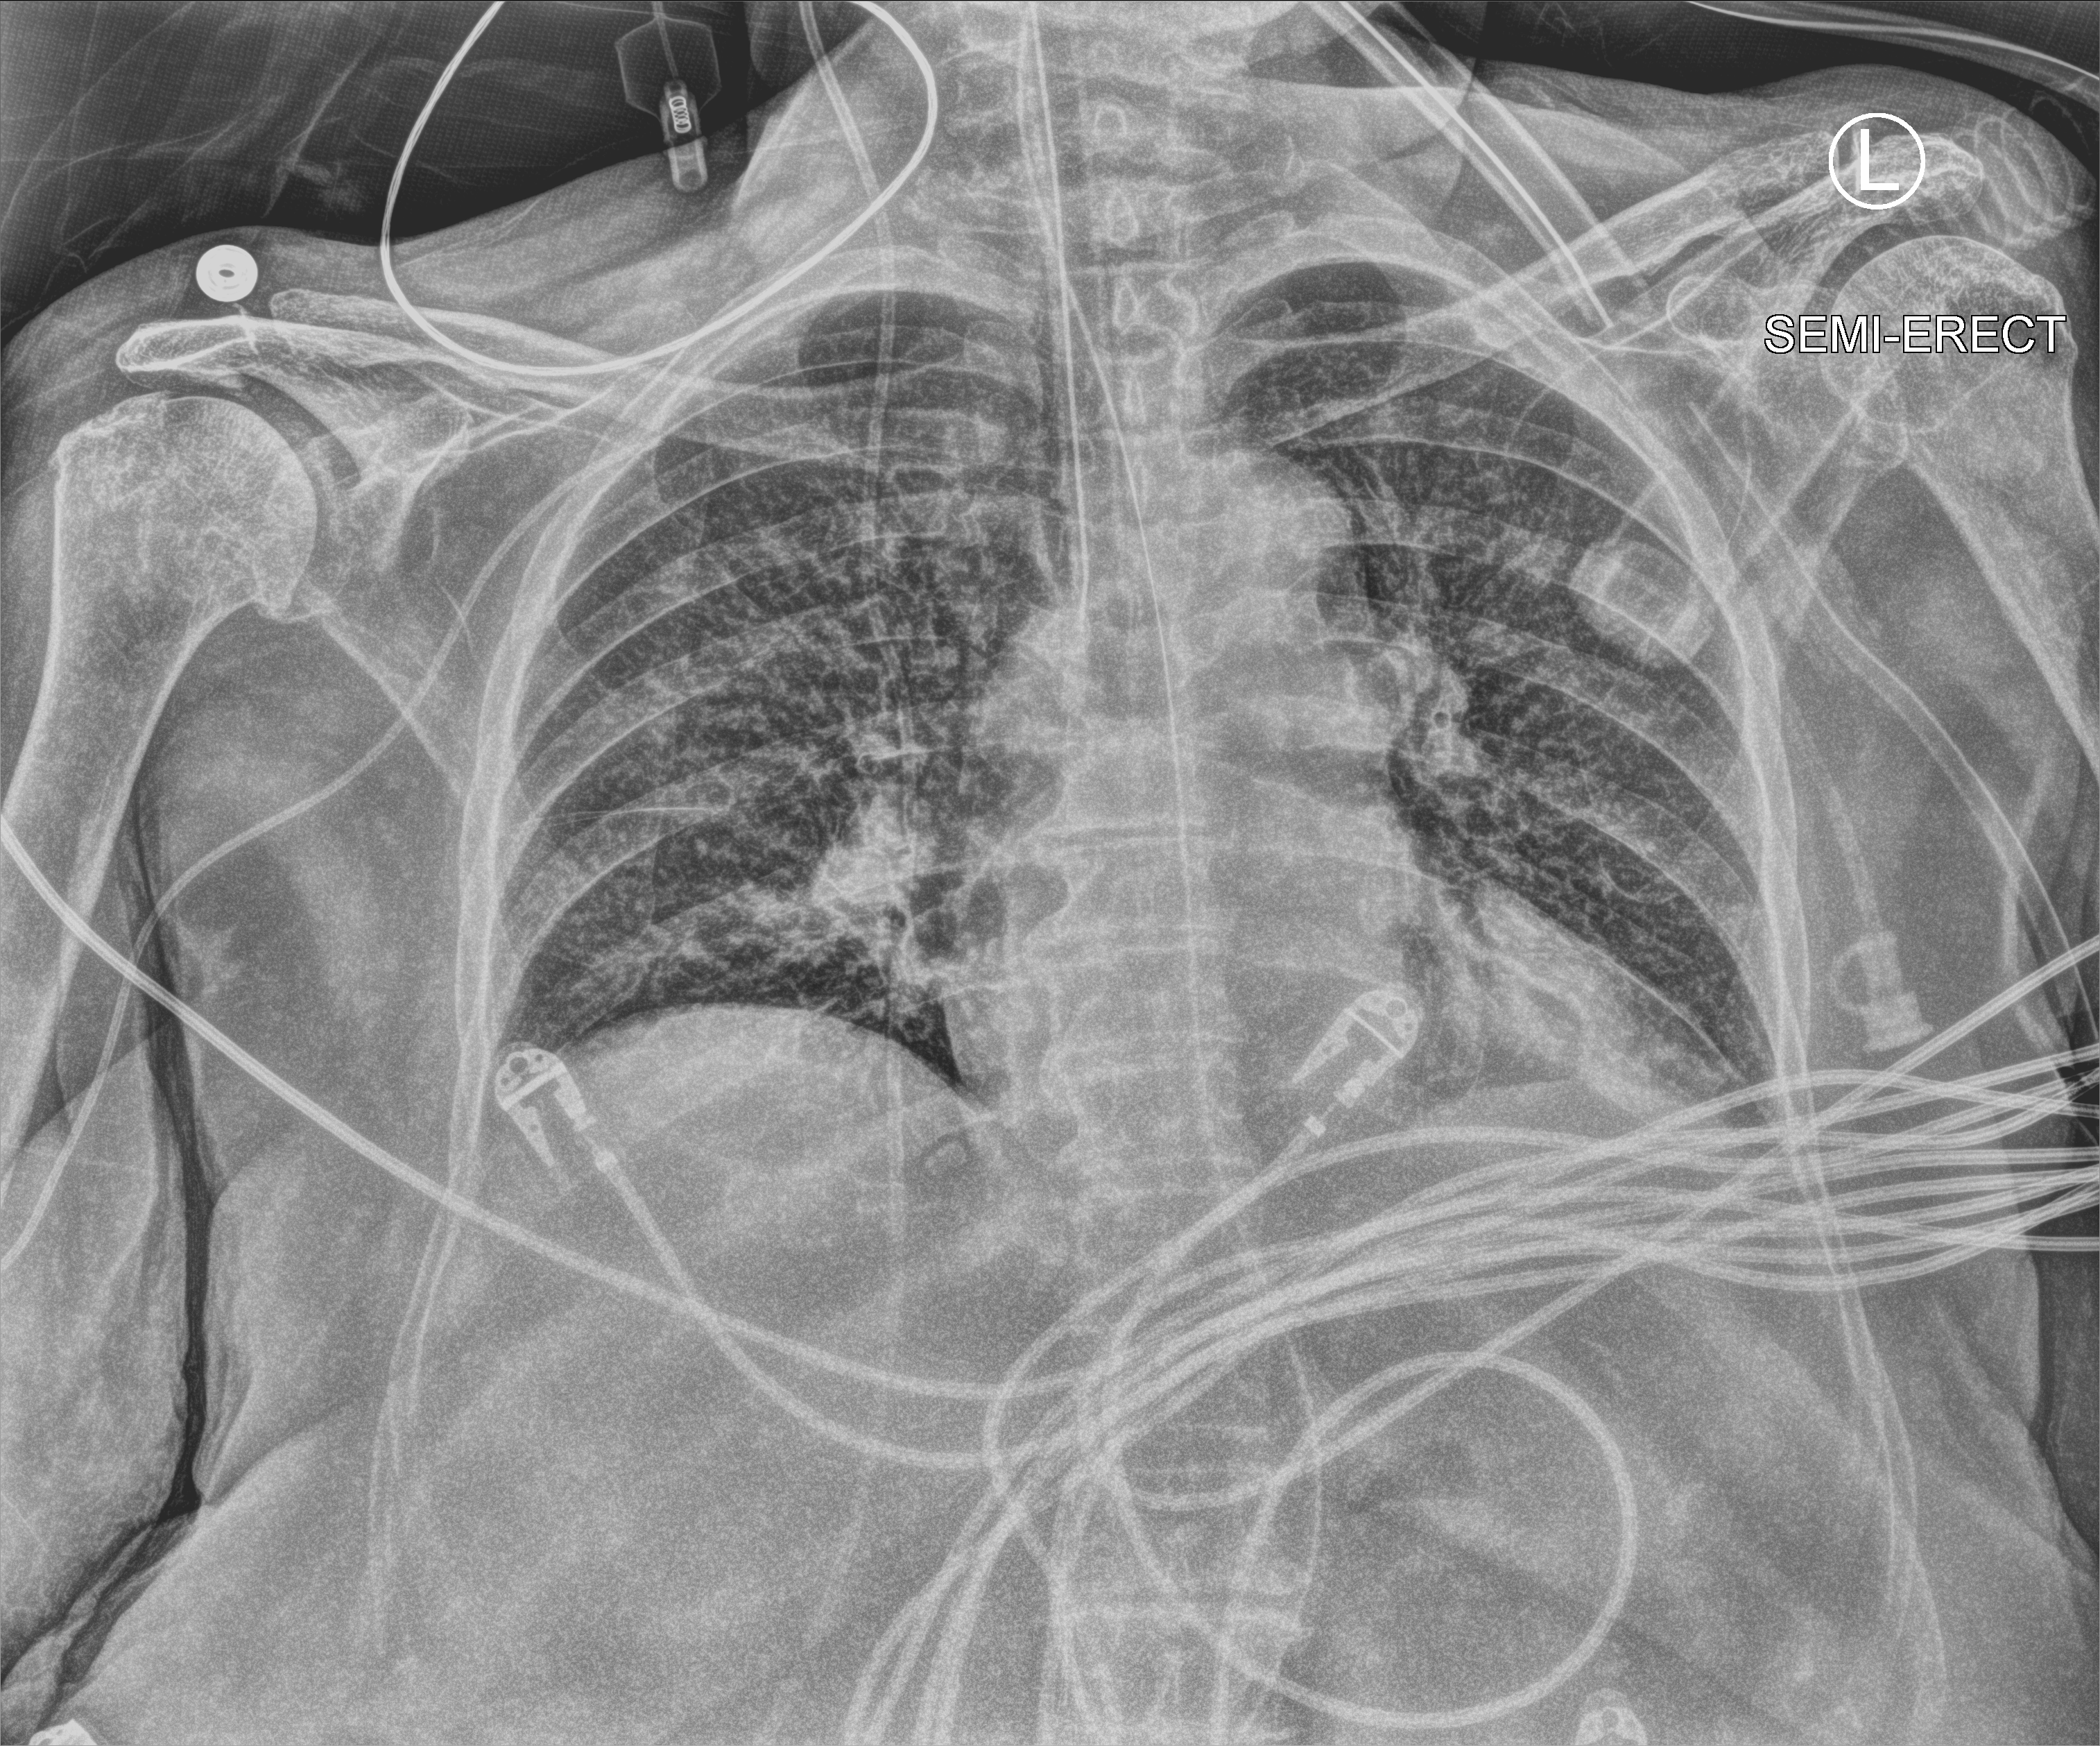
Portable chest radiograph. Female patient hospitalised with COVID-19, age 75–90 years.
Admission-level facts for this patient (not findings on this image; timing relative to this image not recorded): mechanically ventilated during this hospital stay: yes.